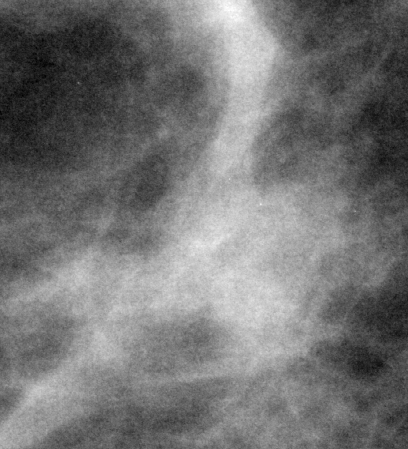
Cropped region of a digitized screen-film mammogram centred on a radiologist-marked abnormality; right breast; MLO view.
Mass, shape irregular, margins ill defined; BI-RADS assessment category 3; subtlety rating 5 on a 1 (subtle) to 5 (obvious) scale; benign; no additional work-up was recommended (benign without callback).